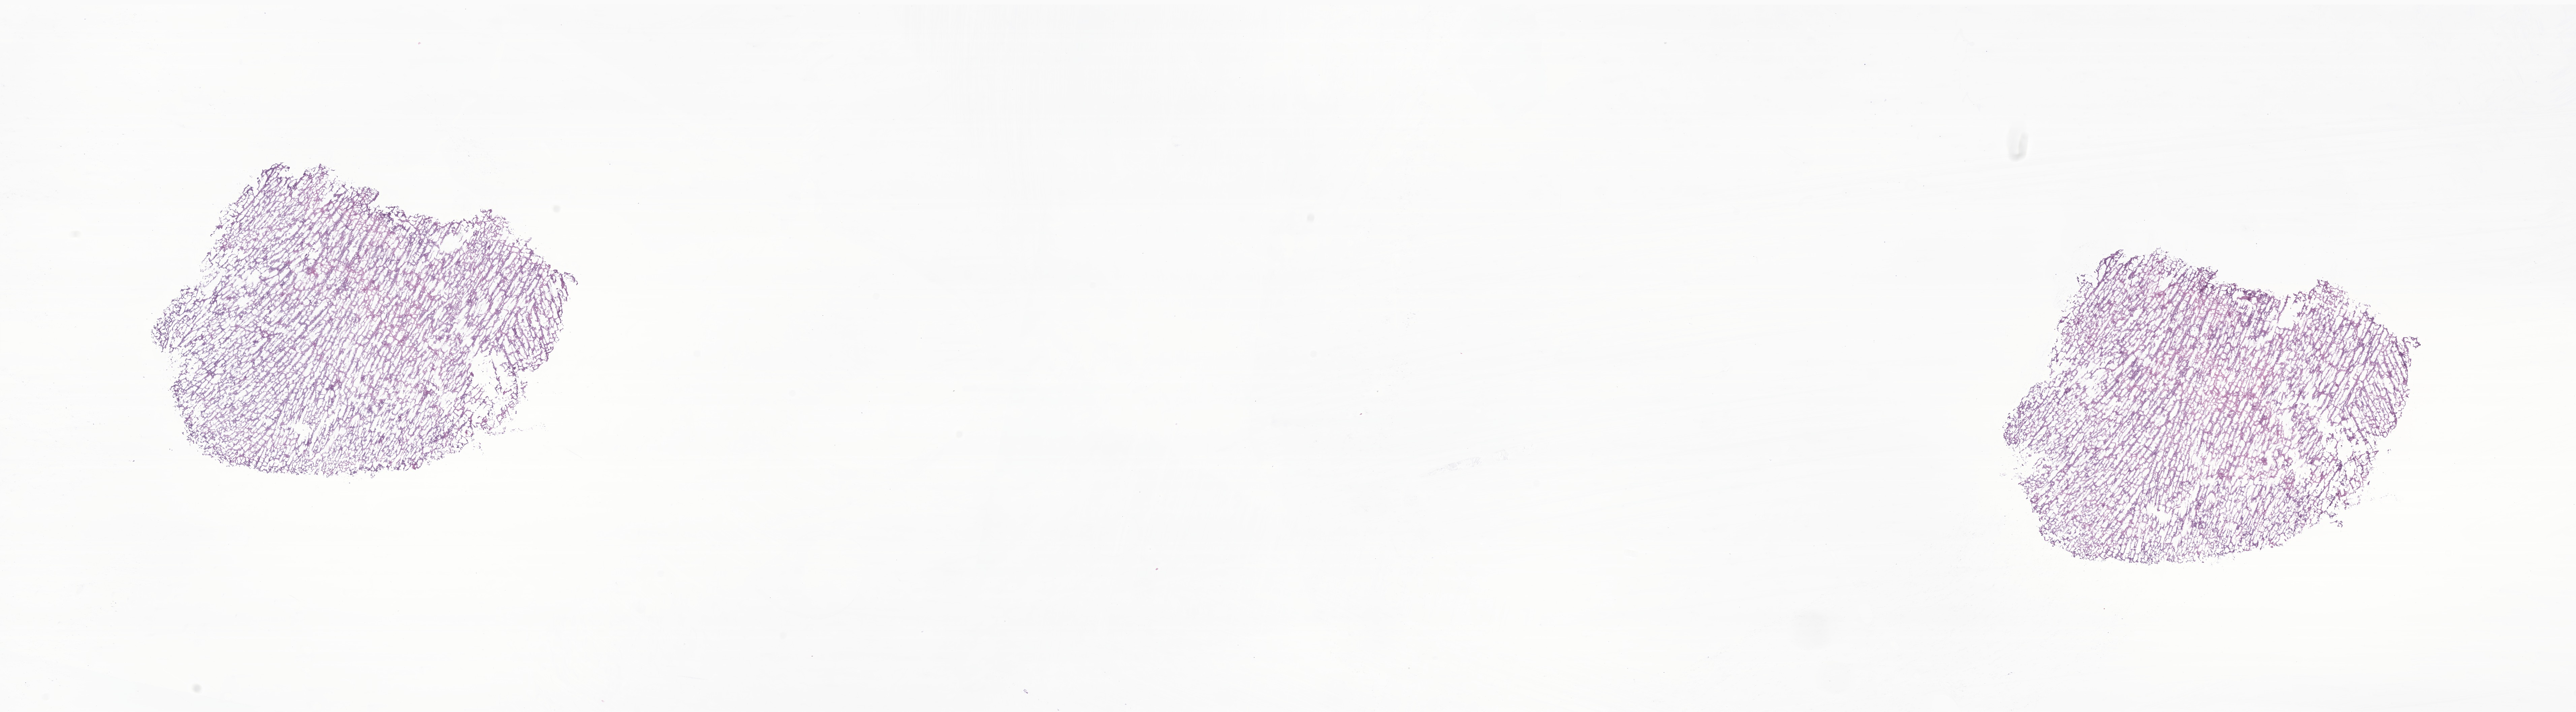
Whole-slide image, haematoxylin and eosin stain of tumor tissue from the brain — whole scanned area (about 32.2 x 8.9 mm) shown as a low-resolution overview; frozen section. Patient male; age 724 days (about 2.0 years).
Diagnosis (ICD-O-3 morphology term): Ependymoma, NOS.